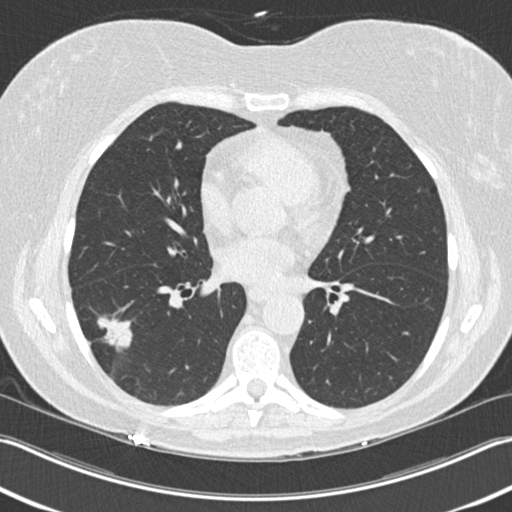
Chest CT (low-dose screening protocol), one axial image. Baseline screening round. Lung window (W 1500 / L -600 HU). Standard (soft-tissue) reconstruction kernel (B30f). Slice 100 of 211 in the series. 512 × 512 image matrix, field of view 348 × 348 mm. Female, age 63 years at enrolment. Current smoker at enrolment.
Expert-annotated lung lesion, bounding box (x1, y1, x2, y2) in pixels: (72, 311, 136, 370). The screening reader recorded 3 non-calcified nodules or masses ≥4 mm on this exam (right upper lobe, right lower lobe, right lower lobe); which of them this box marks is not recorded. Participant outcome: lung cancer diagnosed 57 days after this screen — bronchiolo-alveolar adenocarcinoma, NOS, right lower lobe, well differentiated (G1), stage IA (AJCC 6th edition), 25 mm at pathology.